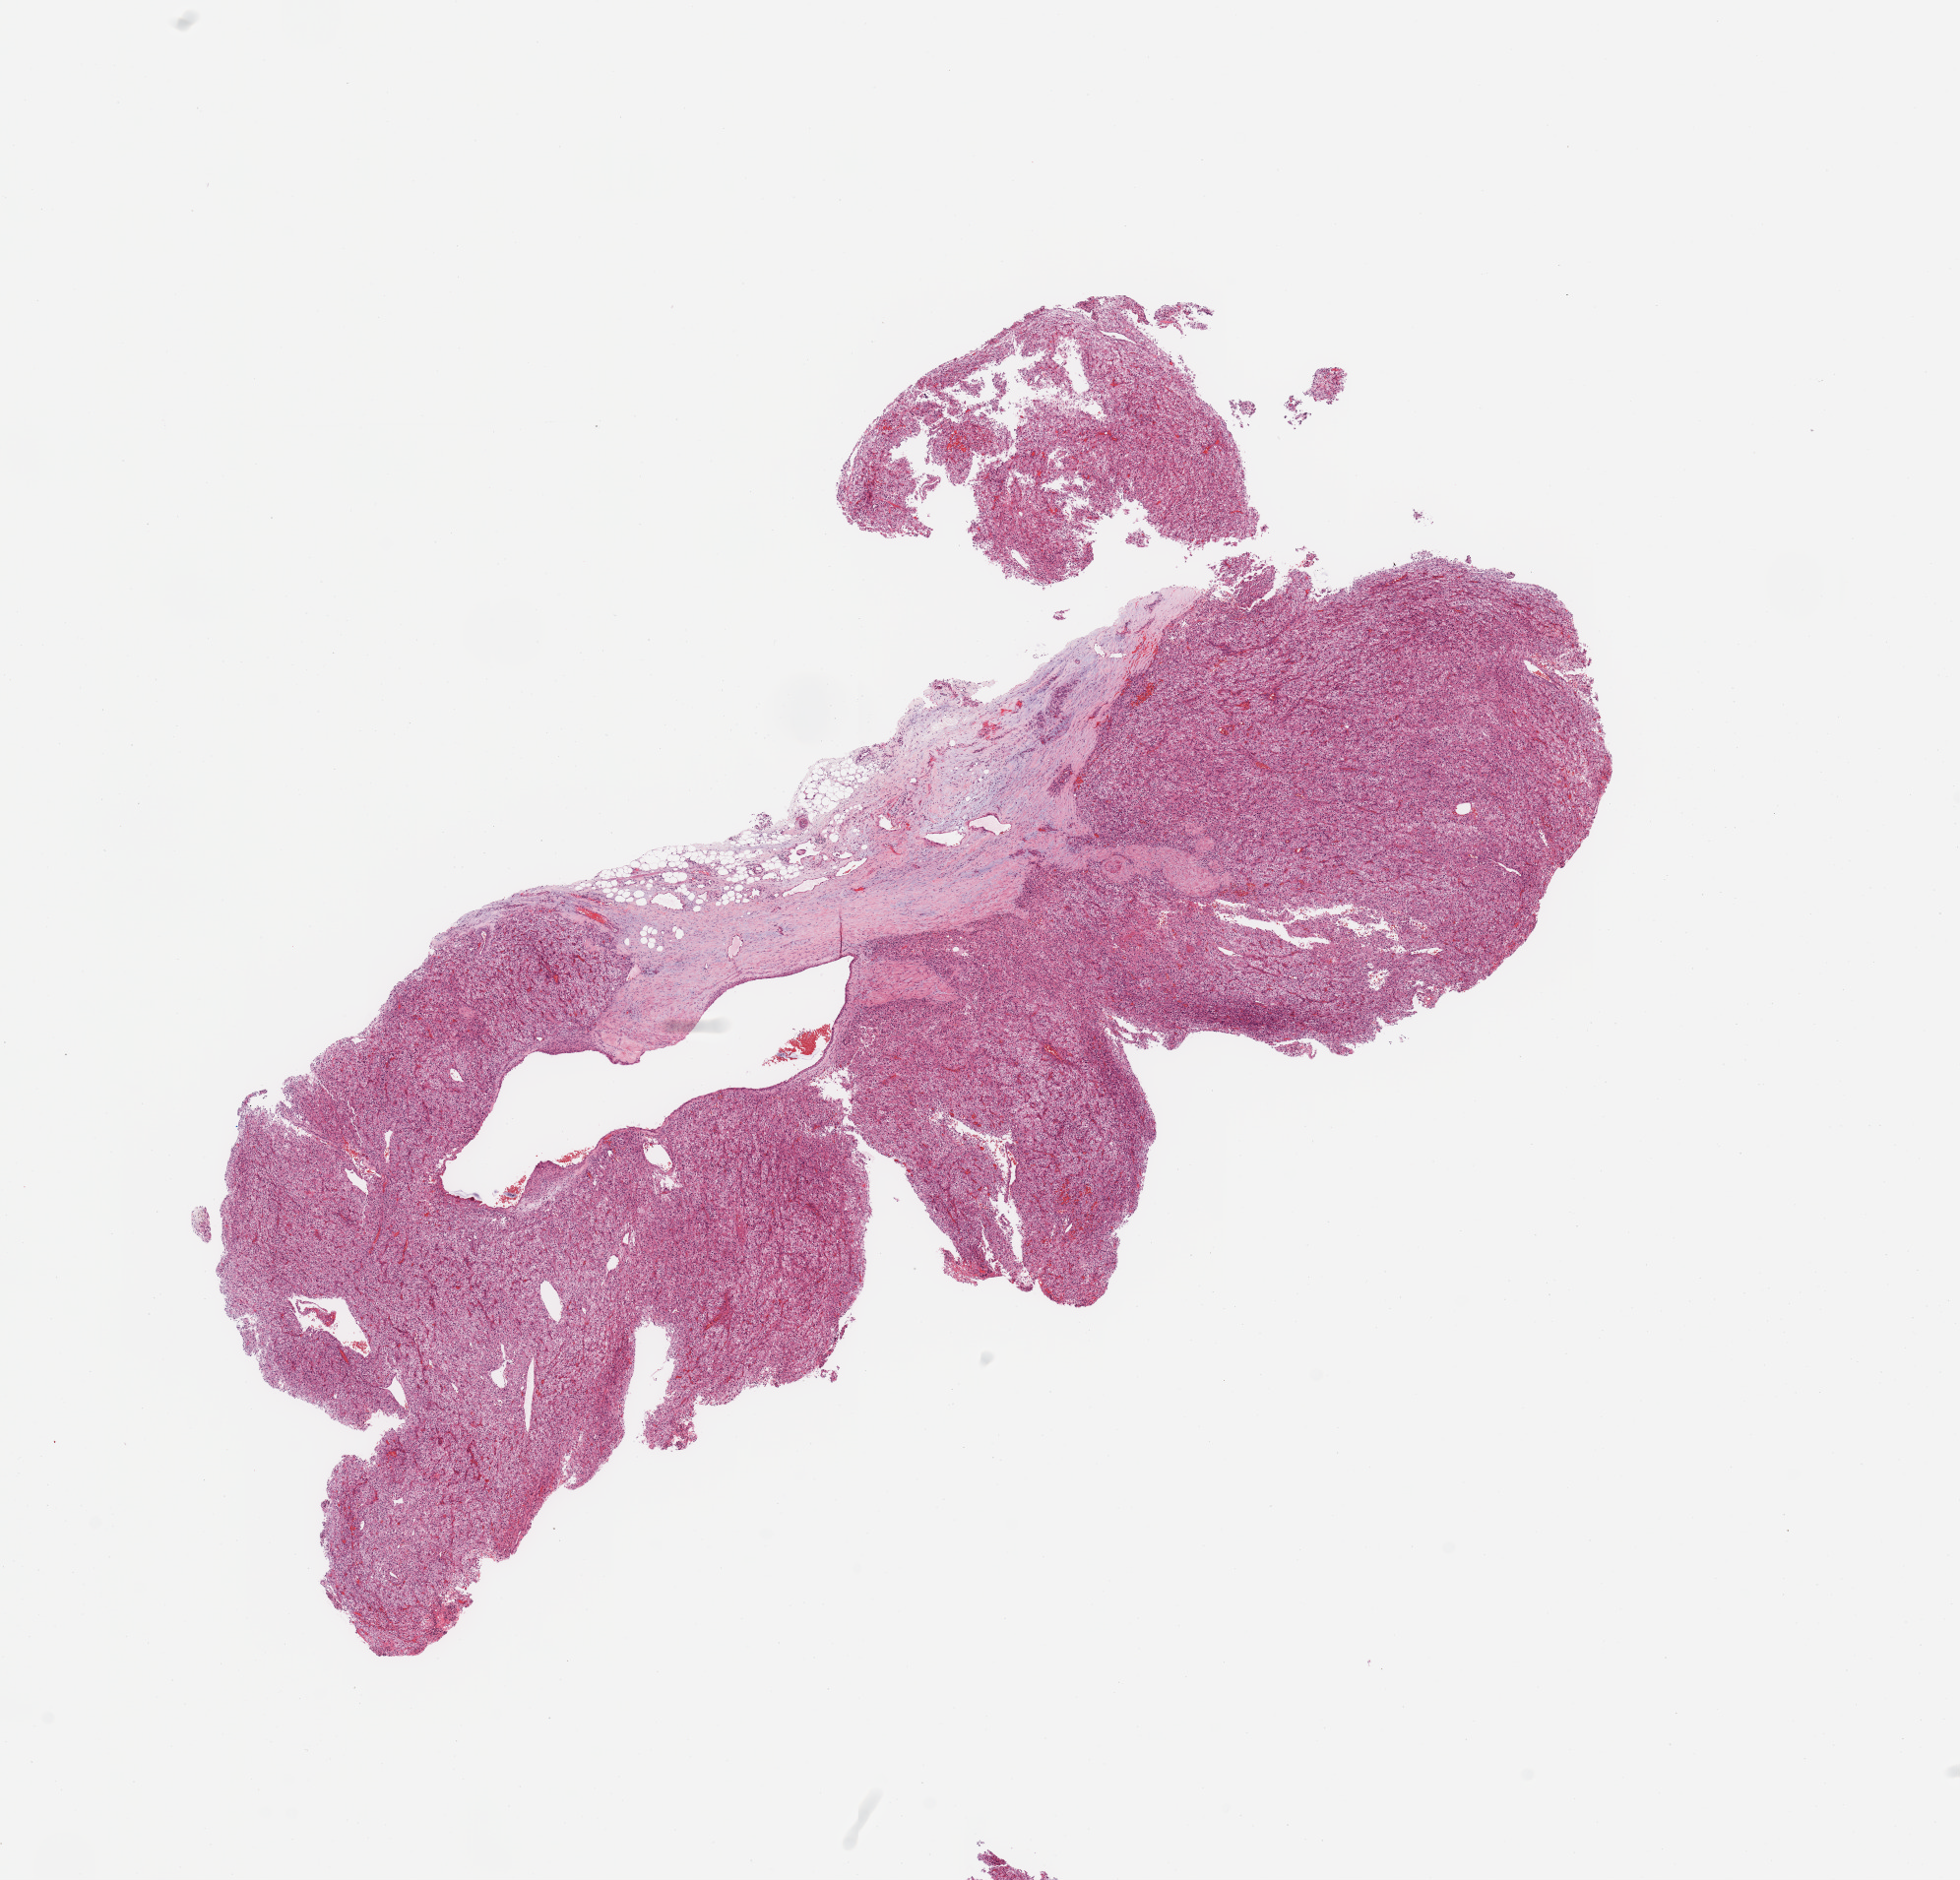
Digitized H&E-stained tissue section (whole slide) — whole scanned area (about 15.8 x 15.1 mm, acquisition: 20x scan) shown as a low-resolution overview; tumour tissue sample, sampled site: kidney. Patient: male, age 58 years. Histologic grade: G3 (poorly differentiated). Composition of this section per pathologist review: tumour nuclei 85%, necrosis 0%.
- diagnosis: Renal cell carcinoma, NOS
- AJCC pathologic stage: III